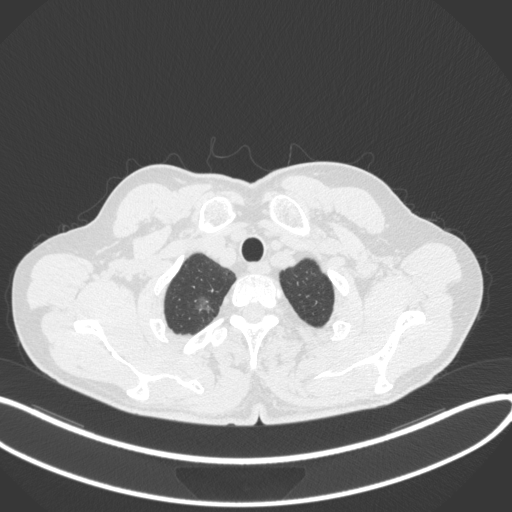
Chest CT, one axial slice; position 354 of 407 along the scan axis; reconstruction kernel B31f; 120 kVp; lung window (W 1500 / L -600 HU); 1 mm slice thickness; 512 × 512 image matrix. Patient: male, 58 years. From the clinical record (not read from this slice): clinical TNM (as recorded): T1c N0 M0.
Structures marked on this image (bounding box drawn by a radiologist):
- lung tumour (recorded histology: adenocarcinoma): bounding box (x1, y1, x2, y2) in pixels: (194, 293, 215, 319)